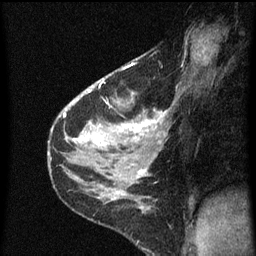
Breast MRI (dynamic contrast-enhanced), one sagittal slice; position 42 of 60 along the scan axis; dynamic contrast-enhanced series, image 2 of 3 at this slice position (ordered by acquisition); 1.5 T; TE 4.2 ms, TR 8 ms; 256 × 256 image matrix, field of view 180 × 180 mm. Patient: female, 38 years.
Annotated regions visible in this slice (semi-automatic segmentation, software-assisted and operator-edited):
- analysis volume of interest (the breast-tissue region the enhancement analysis was run in; not a lesion): box from (x=80, y=54) to (x=169, y=151) px
- tumour enhancement mask (voxels above the 70 % enhancement threshold inside the analysis volume of interest): (x=80, y=80)–(x=165, y=147)